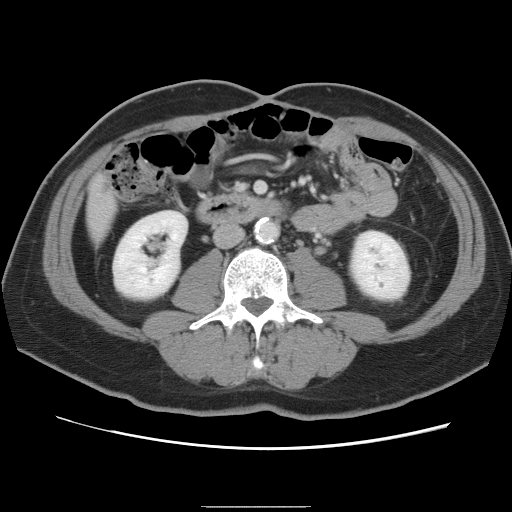
Contrast-enhanced abdominal CT, one axial slice. 120 kVp. Intravenous contrast given. Soft-tissue window (W 400 / L 40 HU). 5 mm slice thickness. 512 × 512 image matrix. Male patient, age 63 years. From the clinical record (not read from this slice): diagnosis: colorectal cancer liver metastases, imaged before liver resection; multiple liver metastases: no; largest metastasis: 9 cm; disease in both lobes: no.
Annotated regions visible in this slice (expert manual segmentation):
- liver: bounding box (x1, y1, x2, y2) in pixels: (88, 175, 117, 239)
- planned liver remnant (the part of the liver to remain after resection): (88, 176, 117, 239)
- liver metastasis: (103, 183, 110, 196)